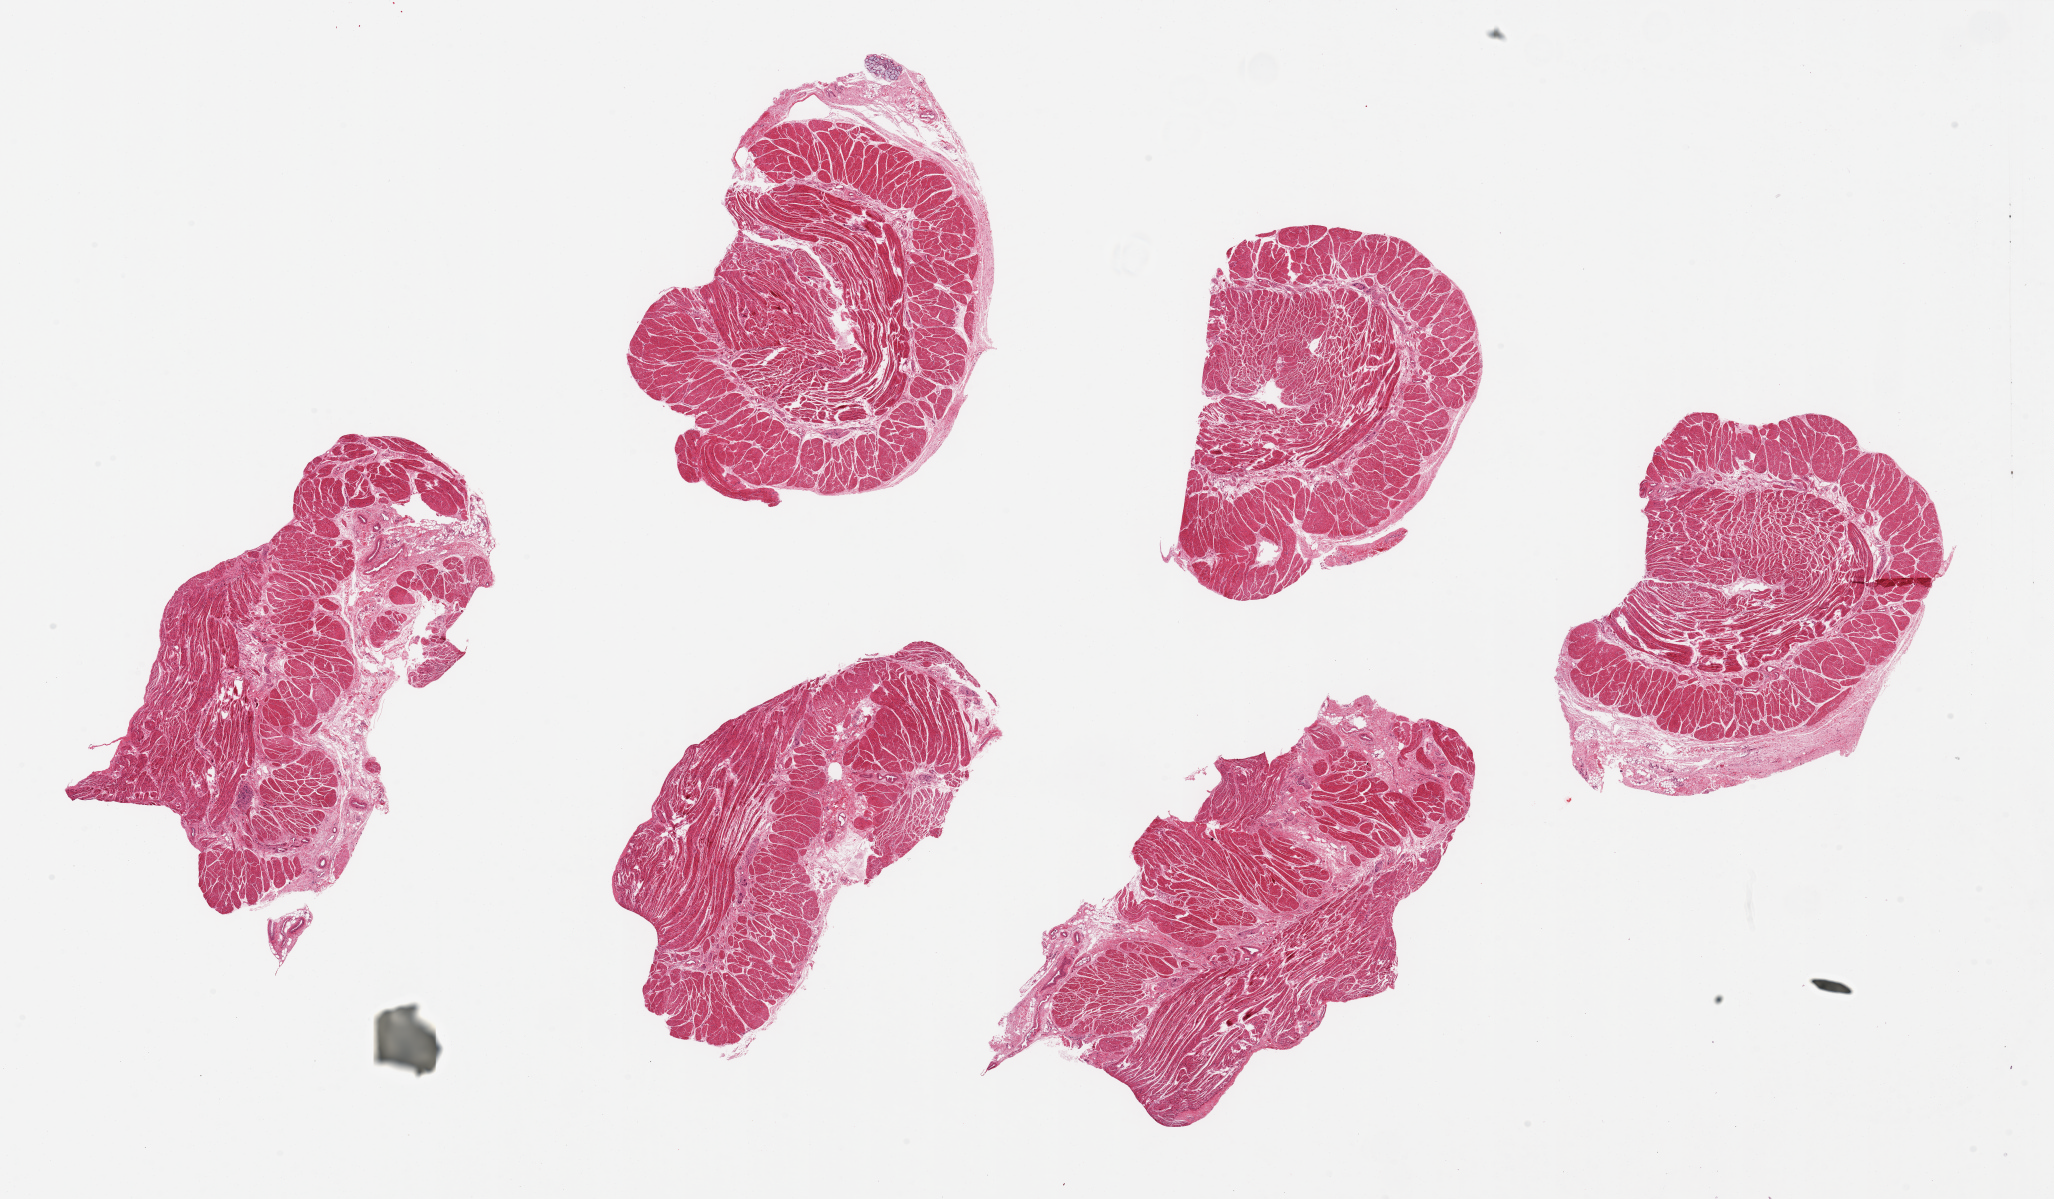
Whole-slide image, haematoxylin and eosin stain — shown as a low-resolution overview of the whole scanned area (about 32.5 x 19.0 mm); PAXgene-fixed paraffin-embedded (PFPE) section; sampled site (target tissue): esophageal muscle; donor tissue sample. Donor sex: female.
• pathologist's review note for this sample: 6 pieces, ~ 7x4mm